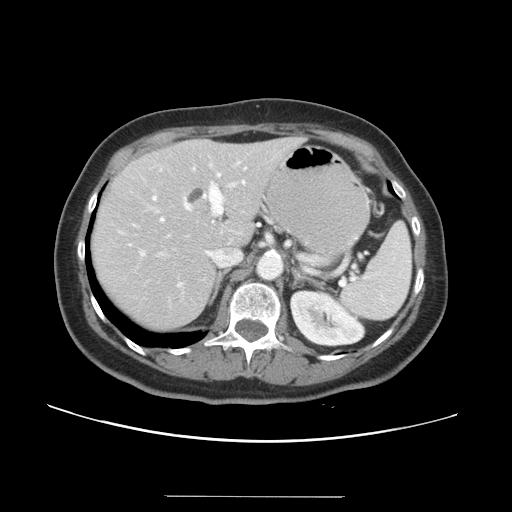
Contrast-enhanced abdominal CT, one axial slice; position 23 of 34 along the scan axis; 120 kVp; intravenous contrast given; soft-tissue window (W 400 / L 40 HU); 5 mm slice thickness; 512 × 512 image matrix, field of view 382 × 382 mm. Female patient, age 69 years. Case-level facts recorded for this patient, not image findings: diagnosis: colorectal cancer liver metastases, imaged before liver resection.
Structures marked on this image (manually delineated by an expert):
- hepatic veins: box from (x=130, y=162) to (x=246, y=287) px
- liver: (x=92, y=138)–(x=304, y=331)
- planned liver remnant (the part of the liver to remain after resection): (x=92, y=138)–(x=304, y=331)
- portal vein (with intrahepatic branches): (x=140, y=174)–(x=354, y=285)
- liver metastasis: (x=185, y=186)–(x=205, y=205)